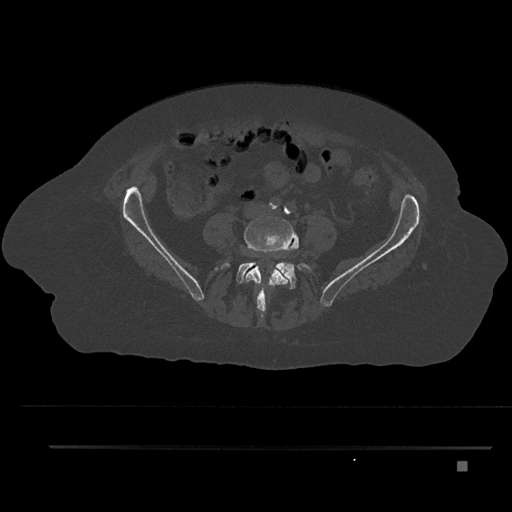
CT including the spine, one axial slice. Position 60 of 797 along the scan axis. Reconstruction kernel Br40s/3. 120 kVp. Bone window (W 1800 / L 400 HU). 0.5 mm slice thickness. 512 × 512 image matrix, field of view 437 × 437 mm. Patient: female, 76 years. Case-level facts recorded for this patient, not image findings: primary cancer: lung; vertebrae with lytic lesions (as recorded): T11, L3.
Annotated regions visible in this slice (semi-automatically segmented with operator editing):
- L4 vertebra: bounding box [x1, y1, x2, y2] px = [244, 216, 298, 314]
- L5 vertebra: [216, 245, 311, 290]